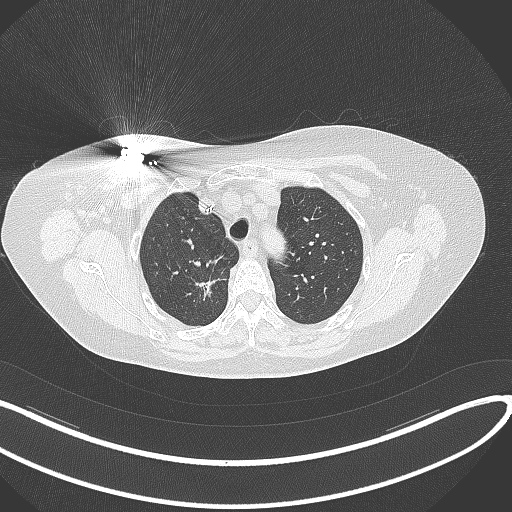
Chest CT, one axial slice. Slice 265 of 316 in the series (ordered by position). Lung window (W 1500 / L -600 HU). 512 × 512 image matrix, field of view 400 × 400 mm. Female patient, age 72 years. From the clinical record (not read from this slice): clinical TNM (as recorded): T1c N0 M0.
Outlined on this slice (rectangle marked by the reading radiologist):
- lung tumour (recorded histology: adenocarcinoma): bounding box <192,271,230,304> (left, top, right, bottom; pixels)